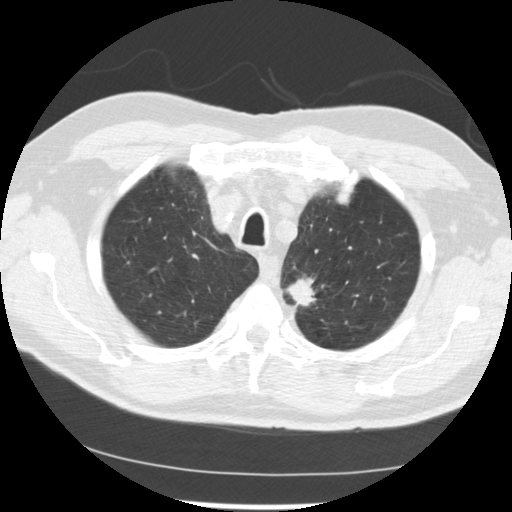
Chest CT (low-dose screening protocol), one axial image; baseline screening round; lung window (W 1500 / L -600 HU); 2.5 mm slice thickness; slice 205 of 249 in the series; 512 × 512 image matrix, field of view 341 × 341 mm. Male participant, aged 71 years at enrolment.
Expert-annotated lung lesion, box from (x=272, y=266) to (x=335, y=318) px. The screening reader recorded 2 non-calcified nodules or masses ≥4 mm on this exam (left upper lobe, left upper lobe); which of them this box marks is not recorded. Later outcome: lung cancer diagnosed 37 days after this screen — adenocarcinoma, NOS, left upper lobe, poorly differentiated (G3), stage IIIB (AJCC 6th edition), 25 mm at pathology.